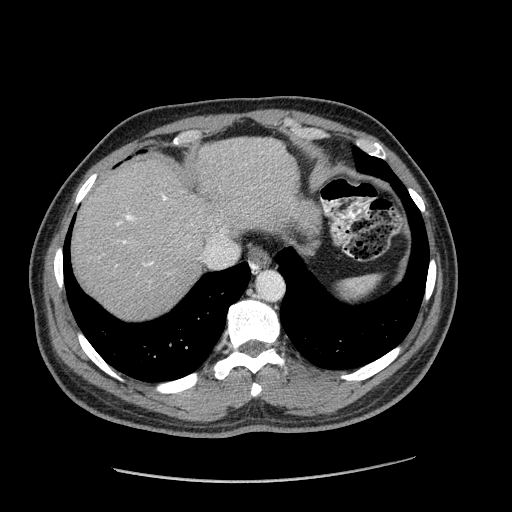
Contrast-enhanced abdominal CT (liver protocol), one axial slice; slice 151 of 182 in the series (ordered by position); 120 kVp; soft-tissue window (W 400 / L 40 HU); 2.5 mm slice thickness; 512 × 512 image matrix, field of view 400 × 400 mm. Case-level facts recorded for this patient, not image findings: diagnosis: hepatocellular carcinoma (patient treated with transarterial chemoembolisation; whether this scan precedes or follows treatment is not stated here); TNM stage (as recorded): Stage-I; Child-Pugh class: A; tumour nodularity: uninodular.
Annotated regions visible in this slice (semi-automatic segmentation, software-assisted and operator-edited):
- abdominal aorta: bounding box [x1, y1, x2, y2] px = [258, 272, 284, 301]
- liver parenchyma outside the tumour (the mass and vessels are separate outlines, so this box may not span the whole liver): [72, 138, 316, 318]
- liver vessels: [117, 195, 167, 266]